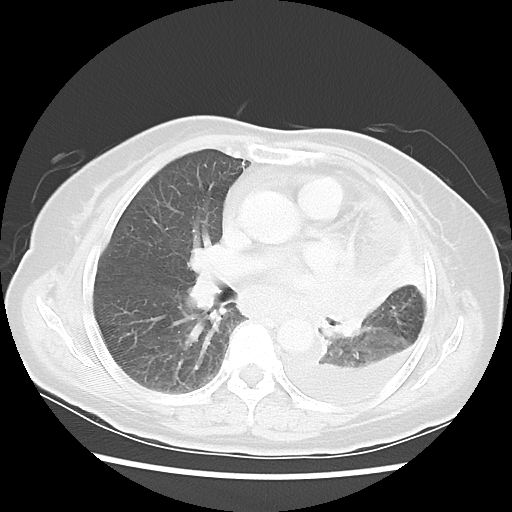
Chest CT, one axial slice; slice 30 of 52 in the series (ordered by position); 120 kVp; lung window (W 1500 / L -600 HU); 512 × 512 image matrix, field of view 336 × 336 mm. Patient: female, 72 years. Case-level facts recorded for this patient, not image findings: clinical TNM (as recorded): T4 N3 M1b.
Outlined on this slice (rectangle marked by the reading radiologist):
- lung tumour (recorded histology: large cell carcinoma): bounding box (x1, y1, x2, y2) in pixels: (295, 264, 392, 353)